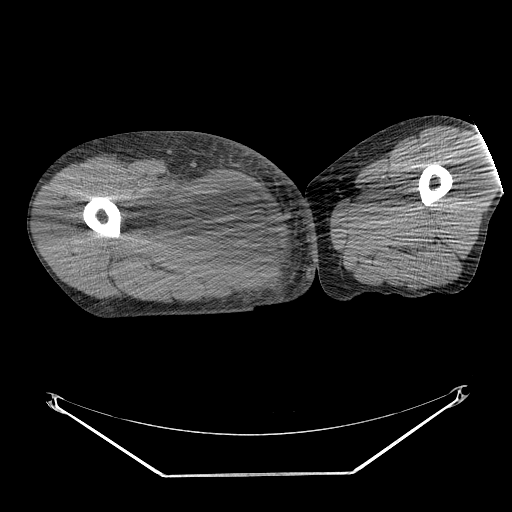
CT of an extremity soft-tissue mass (from a PET/CT study), one axial slice. Slice 247 of 311 in the series (ordered by position). Soft-tissue window (W 400 / L 40 HU). 3.75 mm slice thickness. 512 × 512 image matrix, field of view 500 × 500 mm. Male patient. Case-level facts recorded for this patient, not image findings: histological type: undifferentiated - pleiomorphic; grade: high; site of the primary tumour: right thigh.
Outlined on this slice (expert contour drawn on MRI and transferred to this co-registered scan by the dataset authors):
- gross tumour volume including surrounding oedema: bounding box [x1, y1, x2, y2] px = [132, 174, 245, 257]
- gross tumour volume (mass): [157, 178, 243, 257]